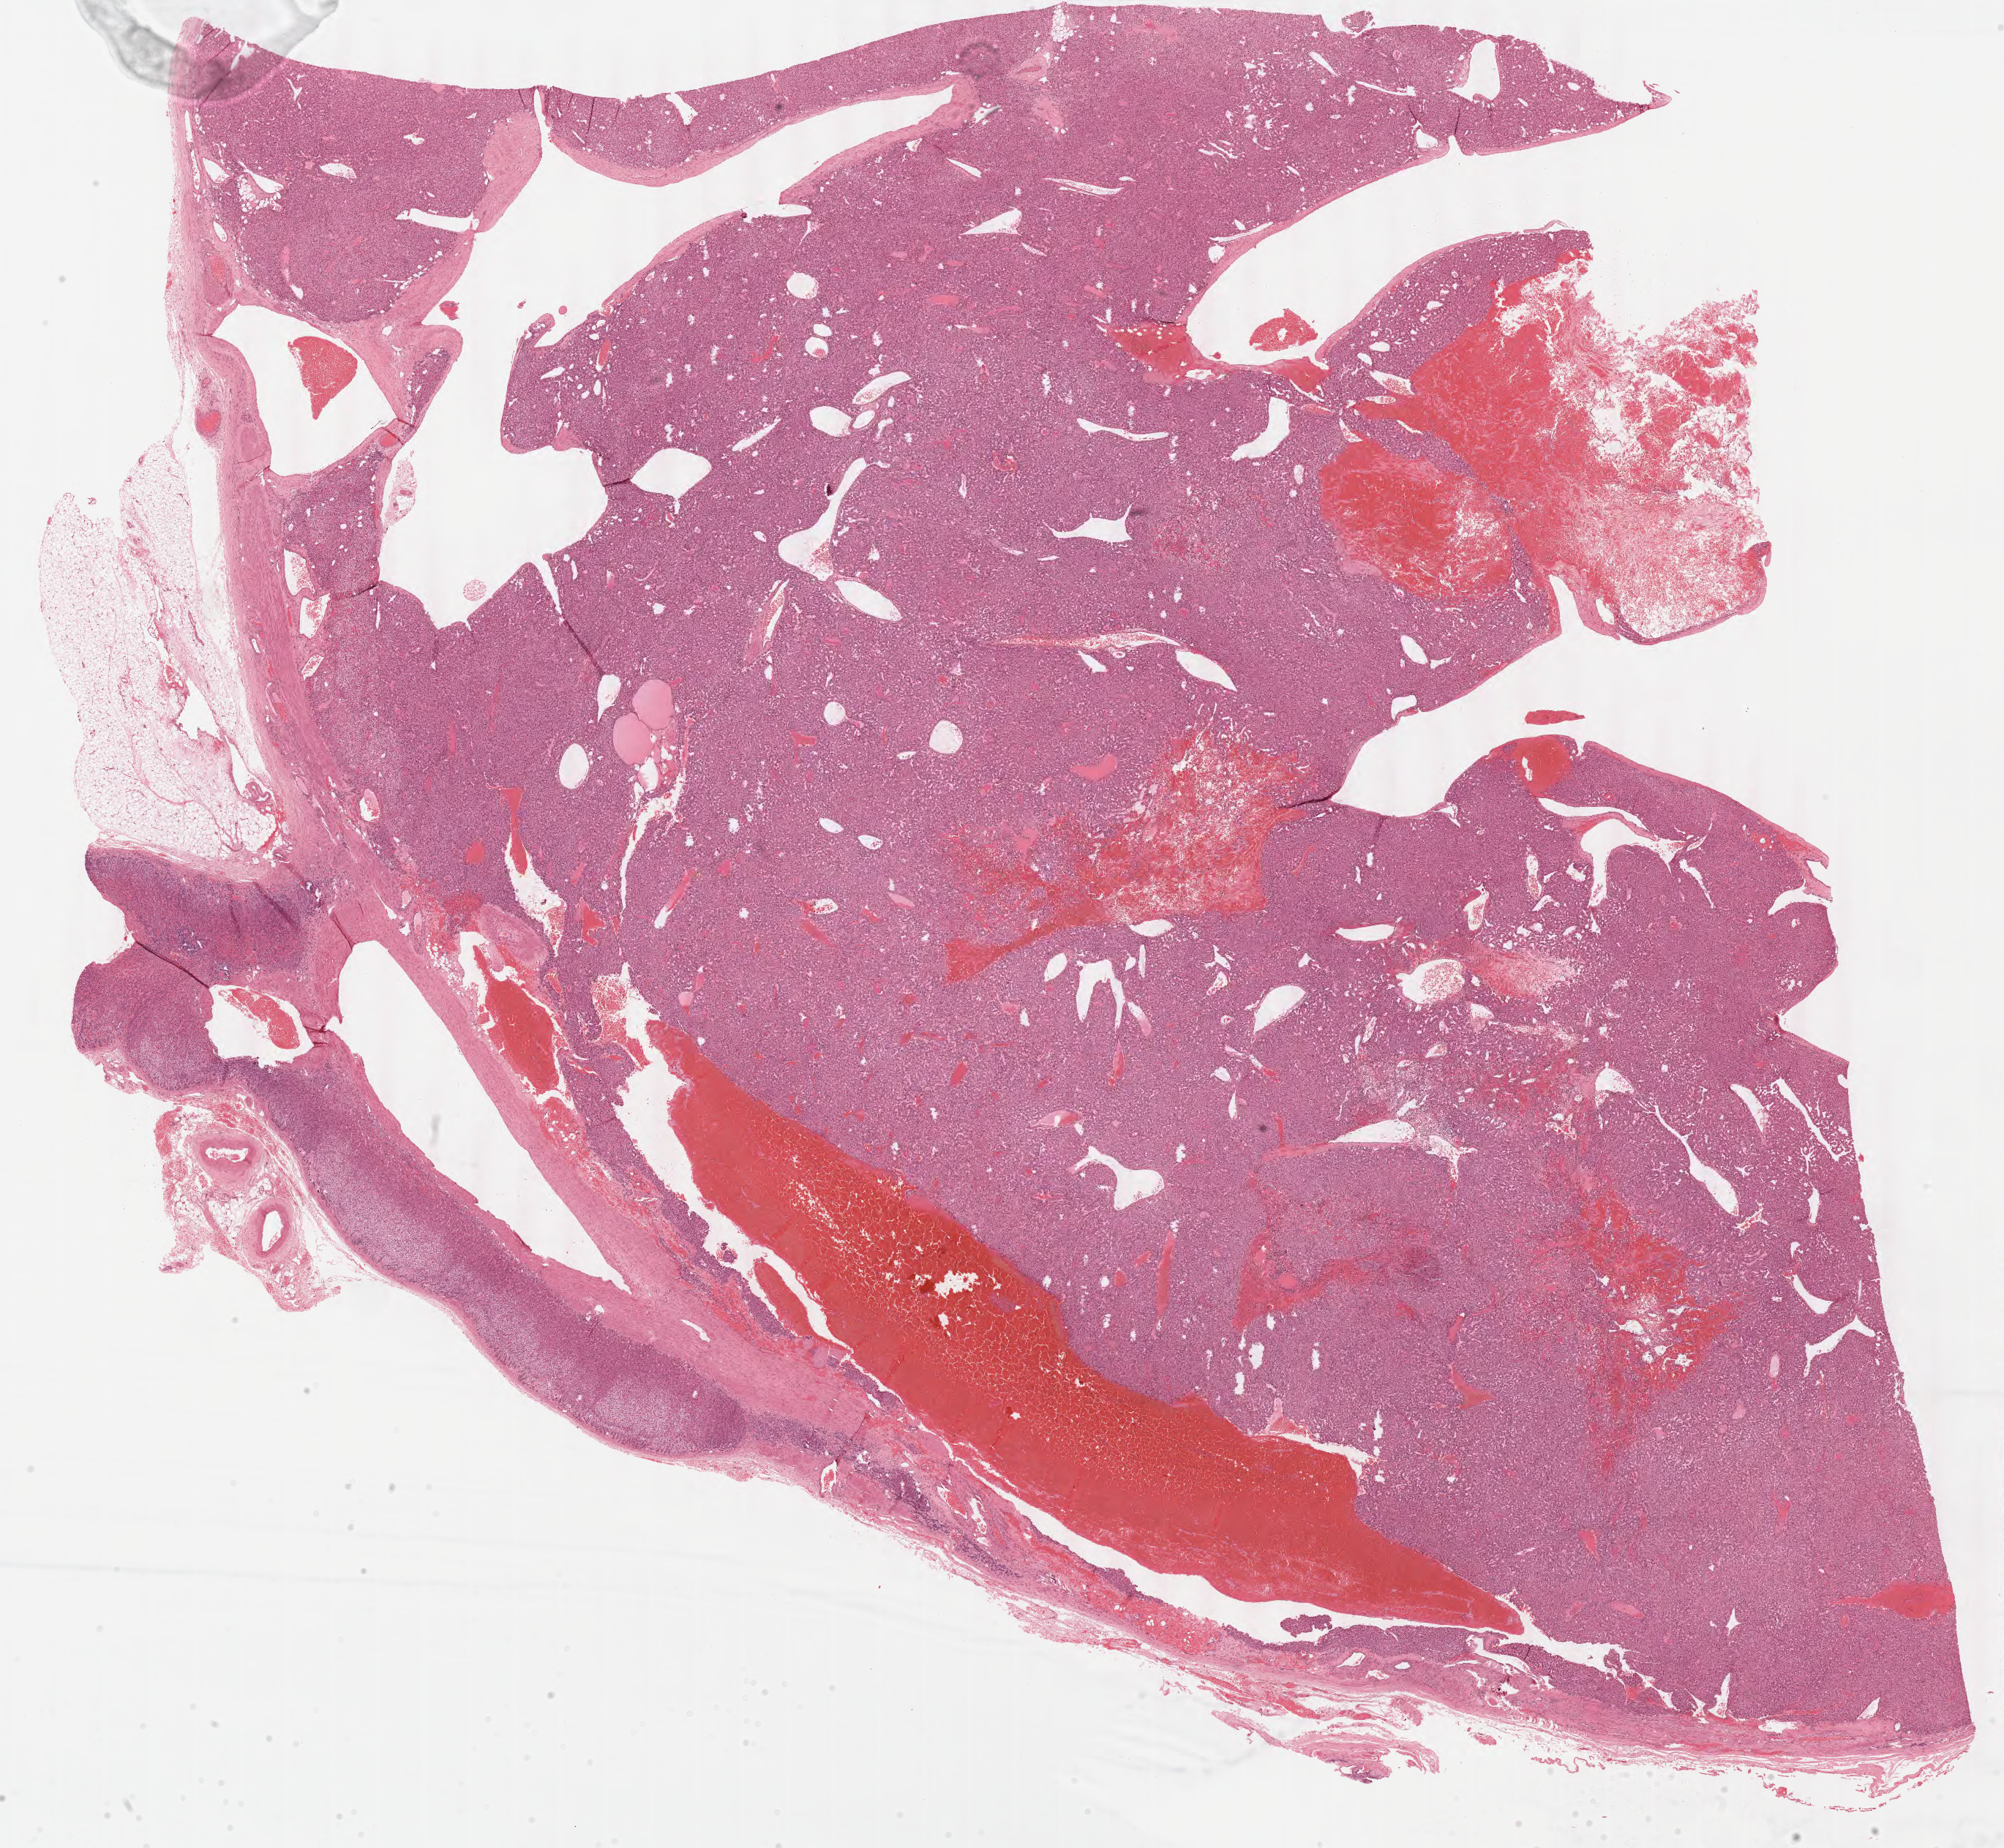
Digitized H&E tissue section (whole slide), shown as a low-resolution overview of the whole scanned area (about 21.6 x 19.9 mm, slide scanned at 40x); FFPE section; adrenal cortex, primary tumour sample. Female patient; age at initial diagnosis 27 years.
- pathologic diagnosis: Adrenal cortical carcinoma (cortex of adrenal gland)
- laterality: right